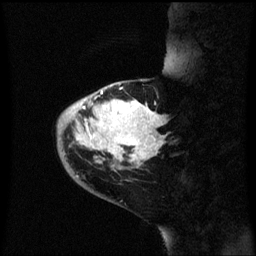
Breast MRI (dynamic contrast-enhanced), one sagittal slice; dynamic contrast-enhanced series, image 2 of 3 at this slice position (ordered by acquisition); 1.5 T; TE 4.2 ms, TR 8.4 ms; 2.3 mm slice thickness; 256 × 256 image matrix, field of view 200 × 200 mm. Patient: female, 46 years. From the clinical record (not read from this slice): setting: breast cancer imaged before/during neoadjuvant chemotherapy; receptor status: HER2-positive.
Outlined on this slice (semi-automatic segmentation, software-assisted and operator-edited):
- analysis volume of interest (the breast-tissue region the enhancement analysis was run in; not a lesion): bounding box <58,86,169,171> (left, top, right, bottom; pixels)
- tumour enhancement mask (voxels above the 70 % enhancement threshold inside the analysis volume of interest): <74,90,163,165>